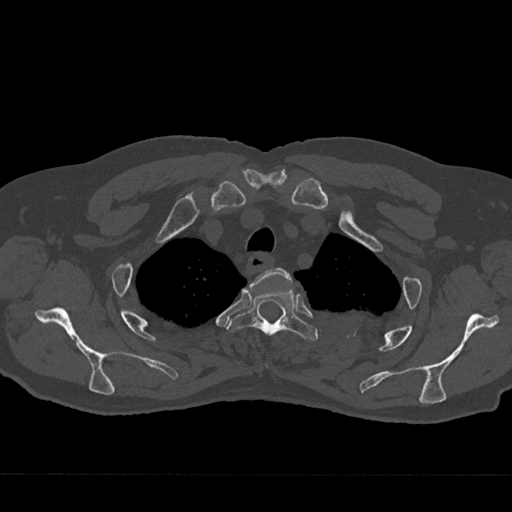
CT including the spine, one axial slice; position 578 of 797 along the scan axis; 120 kVp; bone window (W 1800 / L 400 HU); 0.5 mm slice thickness; 512 × 512 image matrix. Patient: male, 75 years. Case-level facts recorded for this patient, not image findings: primary cancer: renal; vertebrae with lytic lesions (as recorded): T4.
Outlined on this slice (semi-automatically segmented with operator editing):
- T2 vertebra: bounding box <249,268,291,367> (left, top, right, bottom; pixels)
- T3 vertebra: <228,286,317,341>